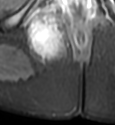
MRI of an extremity soft-tissue mass, one axial slice; slice 31 of 49 in the series (ordered by position); STIR; MR volume resampled by the dataset authors to the PET/CT grid (not the native acquisition matrix); 3.27 mm slice thickness; 115 × 125 image matrix. Female patient. From the clinical record (not read from this slice): histological type: epithelioid sarcoma; grade: intermediate; site of the primary tumour: right buttock.
Outlined on this slice (expert contour drawn on MRI and transferred to this co-registered scan by the dataset authors):
- gross tumour volume including surrounding oedema: bounding box [x1, y1, x2, y2] px = [26, 14, 66, 60]
- gross tumour volume (mass): [31, 21, 57, 51]